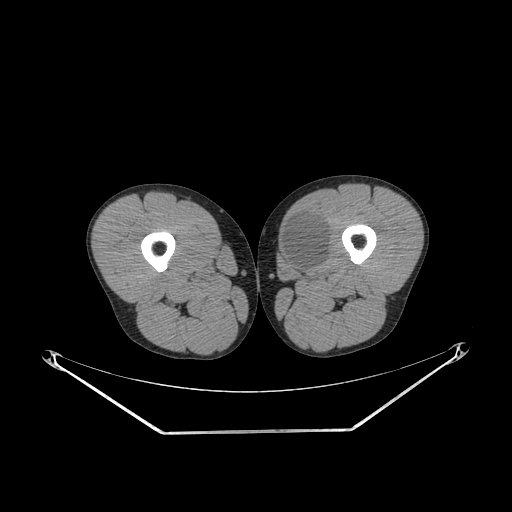
CT of an extremity soft-tissue mass (from a PET/CT study), one axial slice; slice 248 of 311 in the series (ordered by position); soft-tissue window (W 400 / L 40 HU); 3.75 mm slice thickness; 512 × 512 image matrix, field of view 500 × 500 mm. Male patient. From the clinical record (not read from this slice): histological type: mixoid liposarcoma; grade: low; site of the primary tumour: left thigh.
Structures marked on this image (expert contour drawn on MRI and transferred to this co-registered scan by the dataset authors):
- gross tumour volume (mass): bounding box [x1, y1, x2, y2] px = [281, 215, 330, 273]